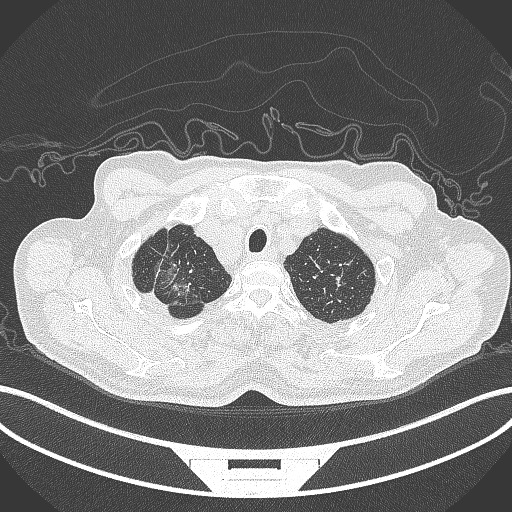
Chest CT, one axial slice. Position 343 of 407 along the scan axis. Reconstruction kernel B70f. 120 kVp. Lung window (W 1500 / L -600 HU). 1 mm slice thickness. 512 × 512 image matrix, field of view 400 × 400 mm. Patient: male, 69 years. Case-level facts recorded for this patient, not image findings: clinical TNM (as recorded): T1c N1 M1.
Outlined on this slice (rectangle marked by the reading radiologist):
- lung tumour (recorded histology: adenocarcinoma): bounding box [x1, y1, x2, y2] px = [144, 253, 202, 313]